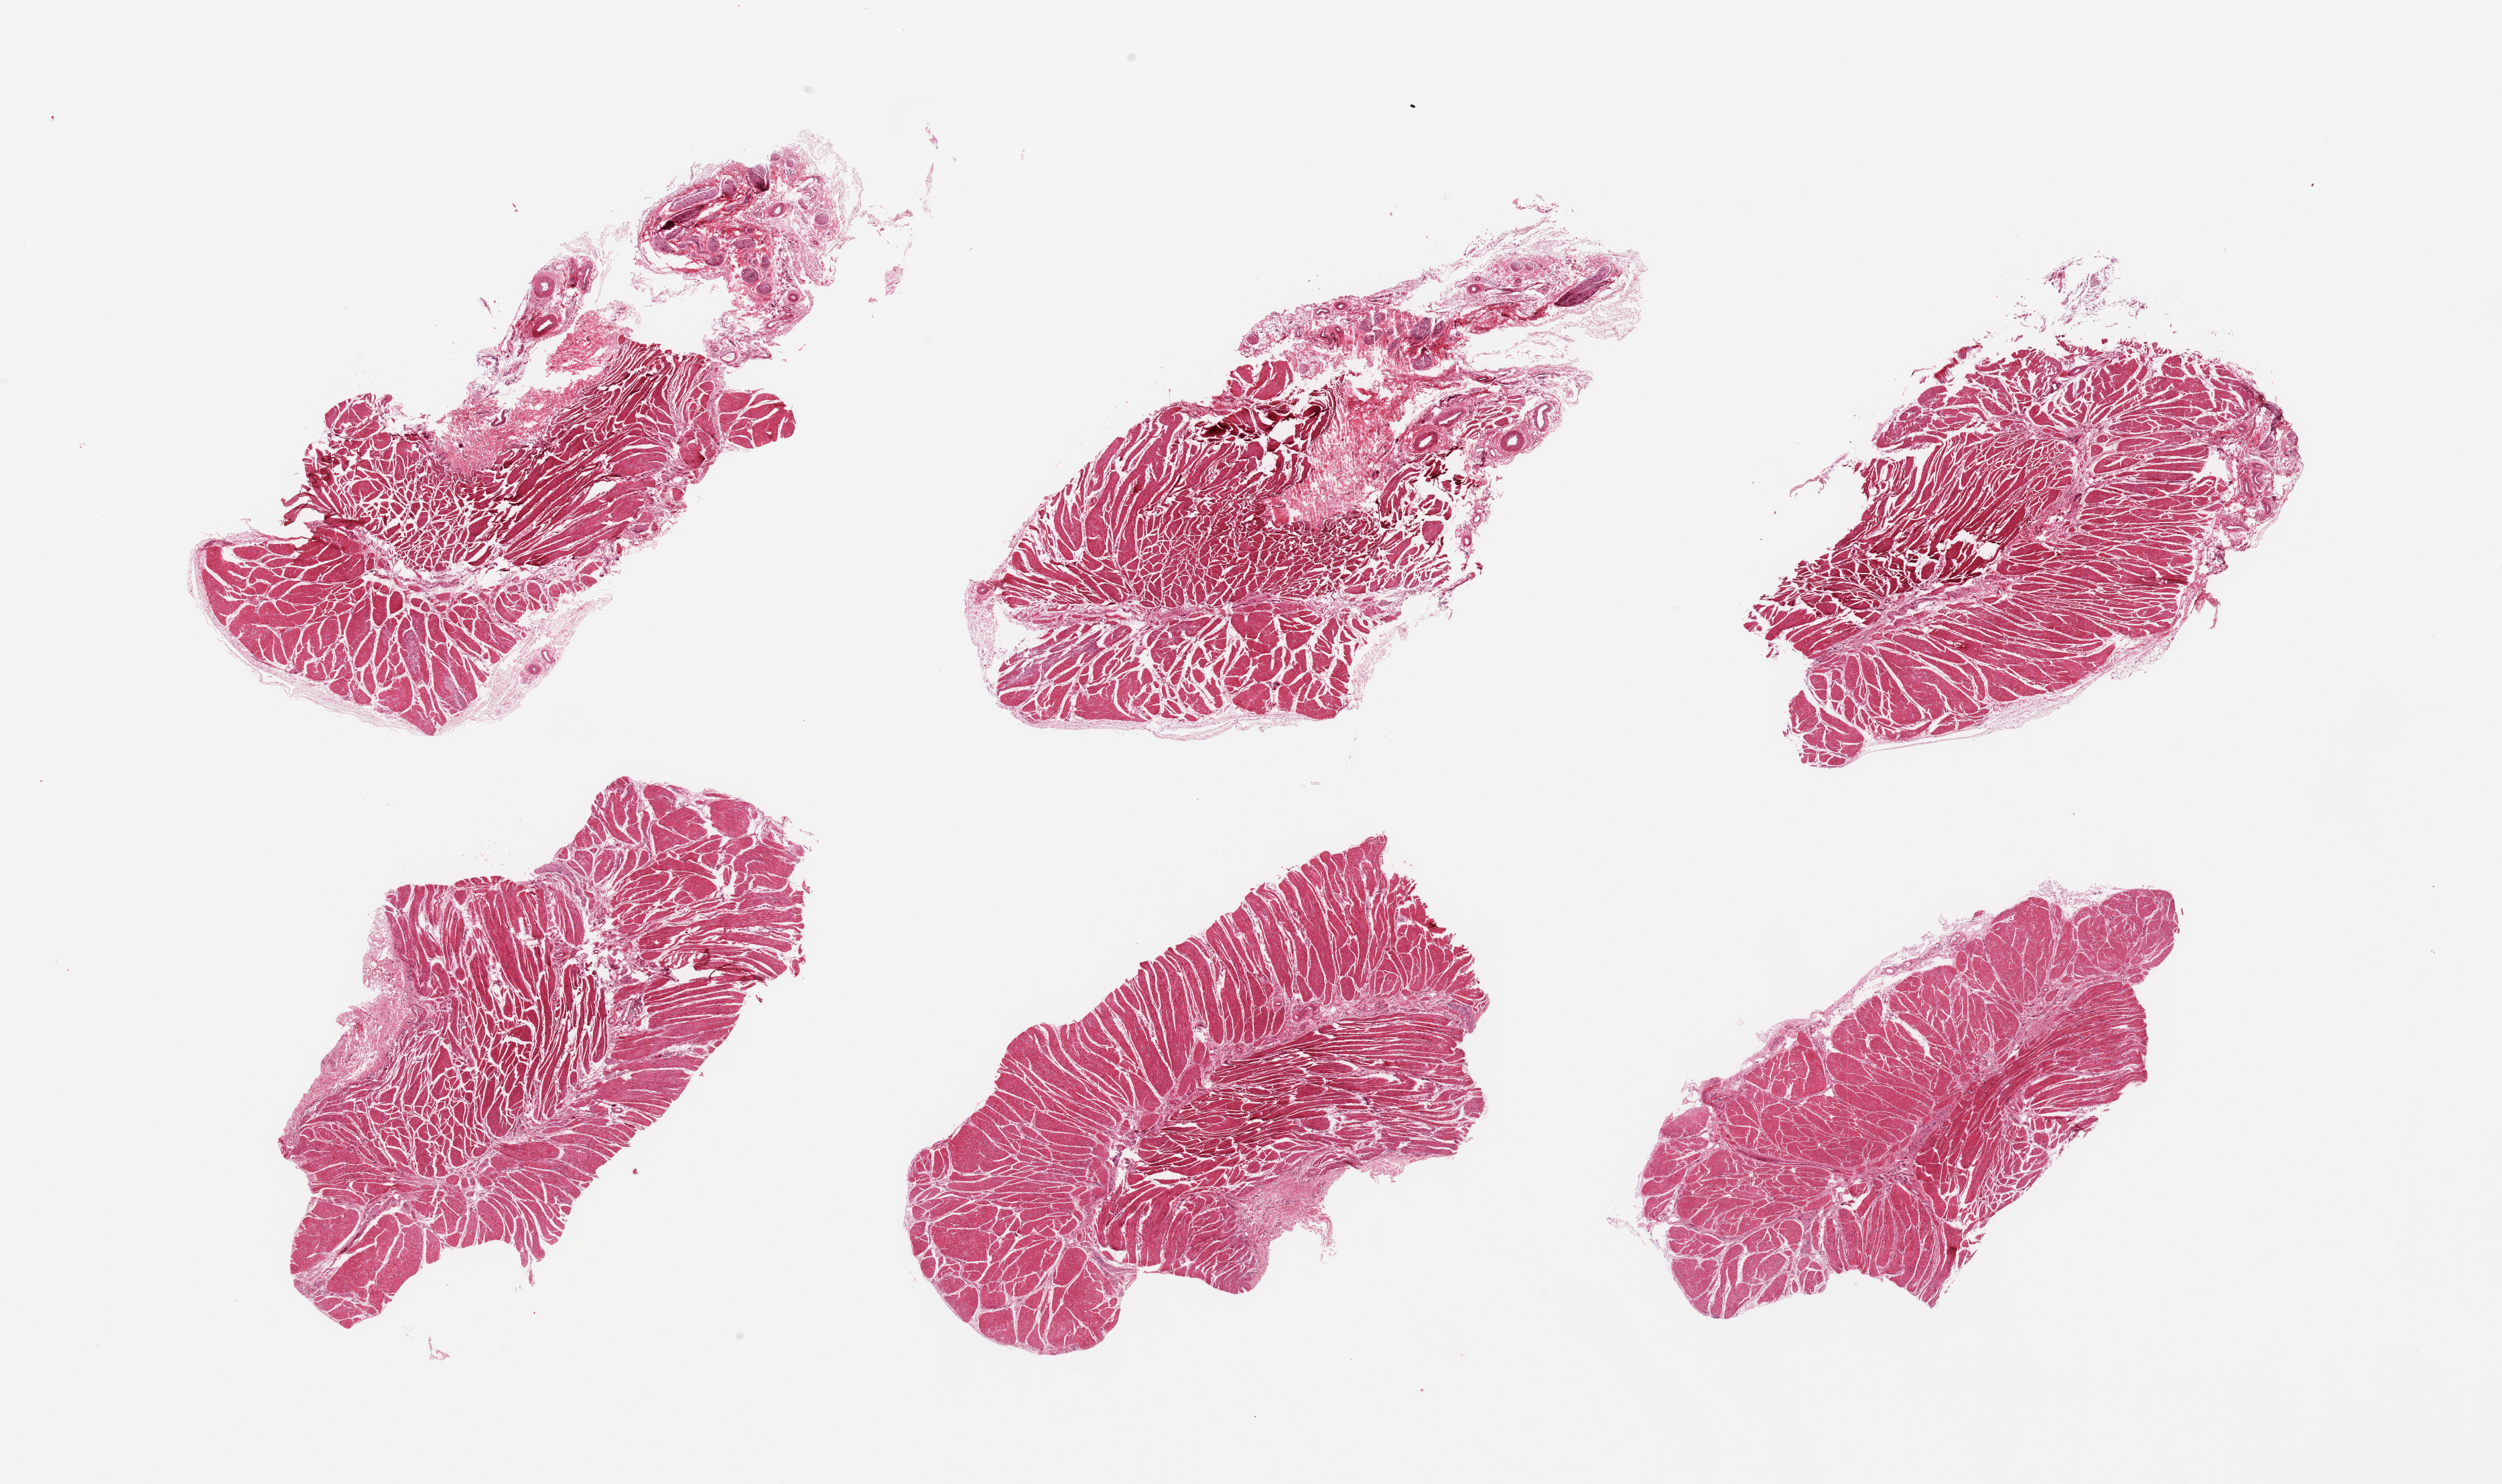
Hematoxylin and eosin (H&E) whole-slide image, a low-resolution overview of the entire scanned area, about 29.5 x 17.5 mm (from a 20x scan); PAXgene-fixed, paraffin-embedded tissue; section of esophageal muscle (target tissue); donor tissue sample.
Reviewer comment on this tissue sample: 6 pieces, confirmed target muscularis.